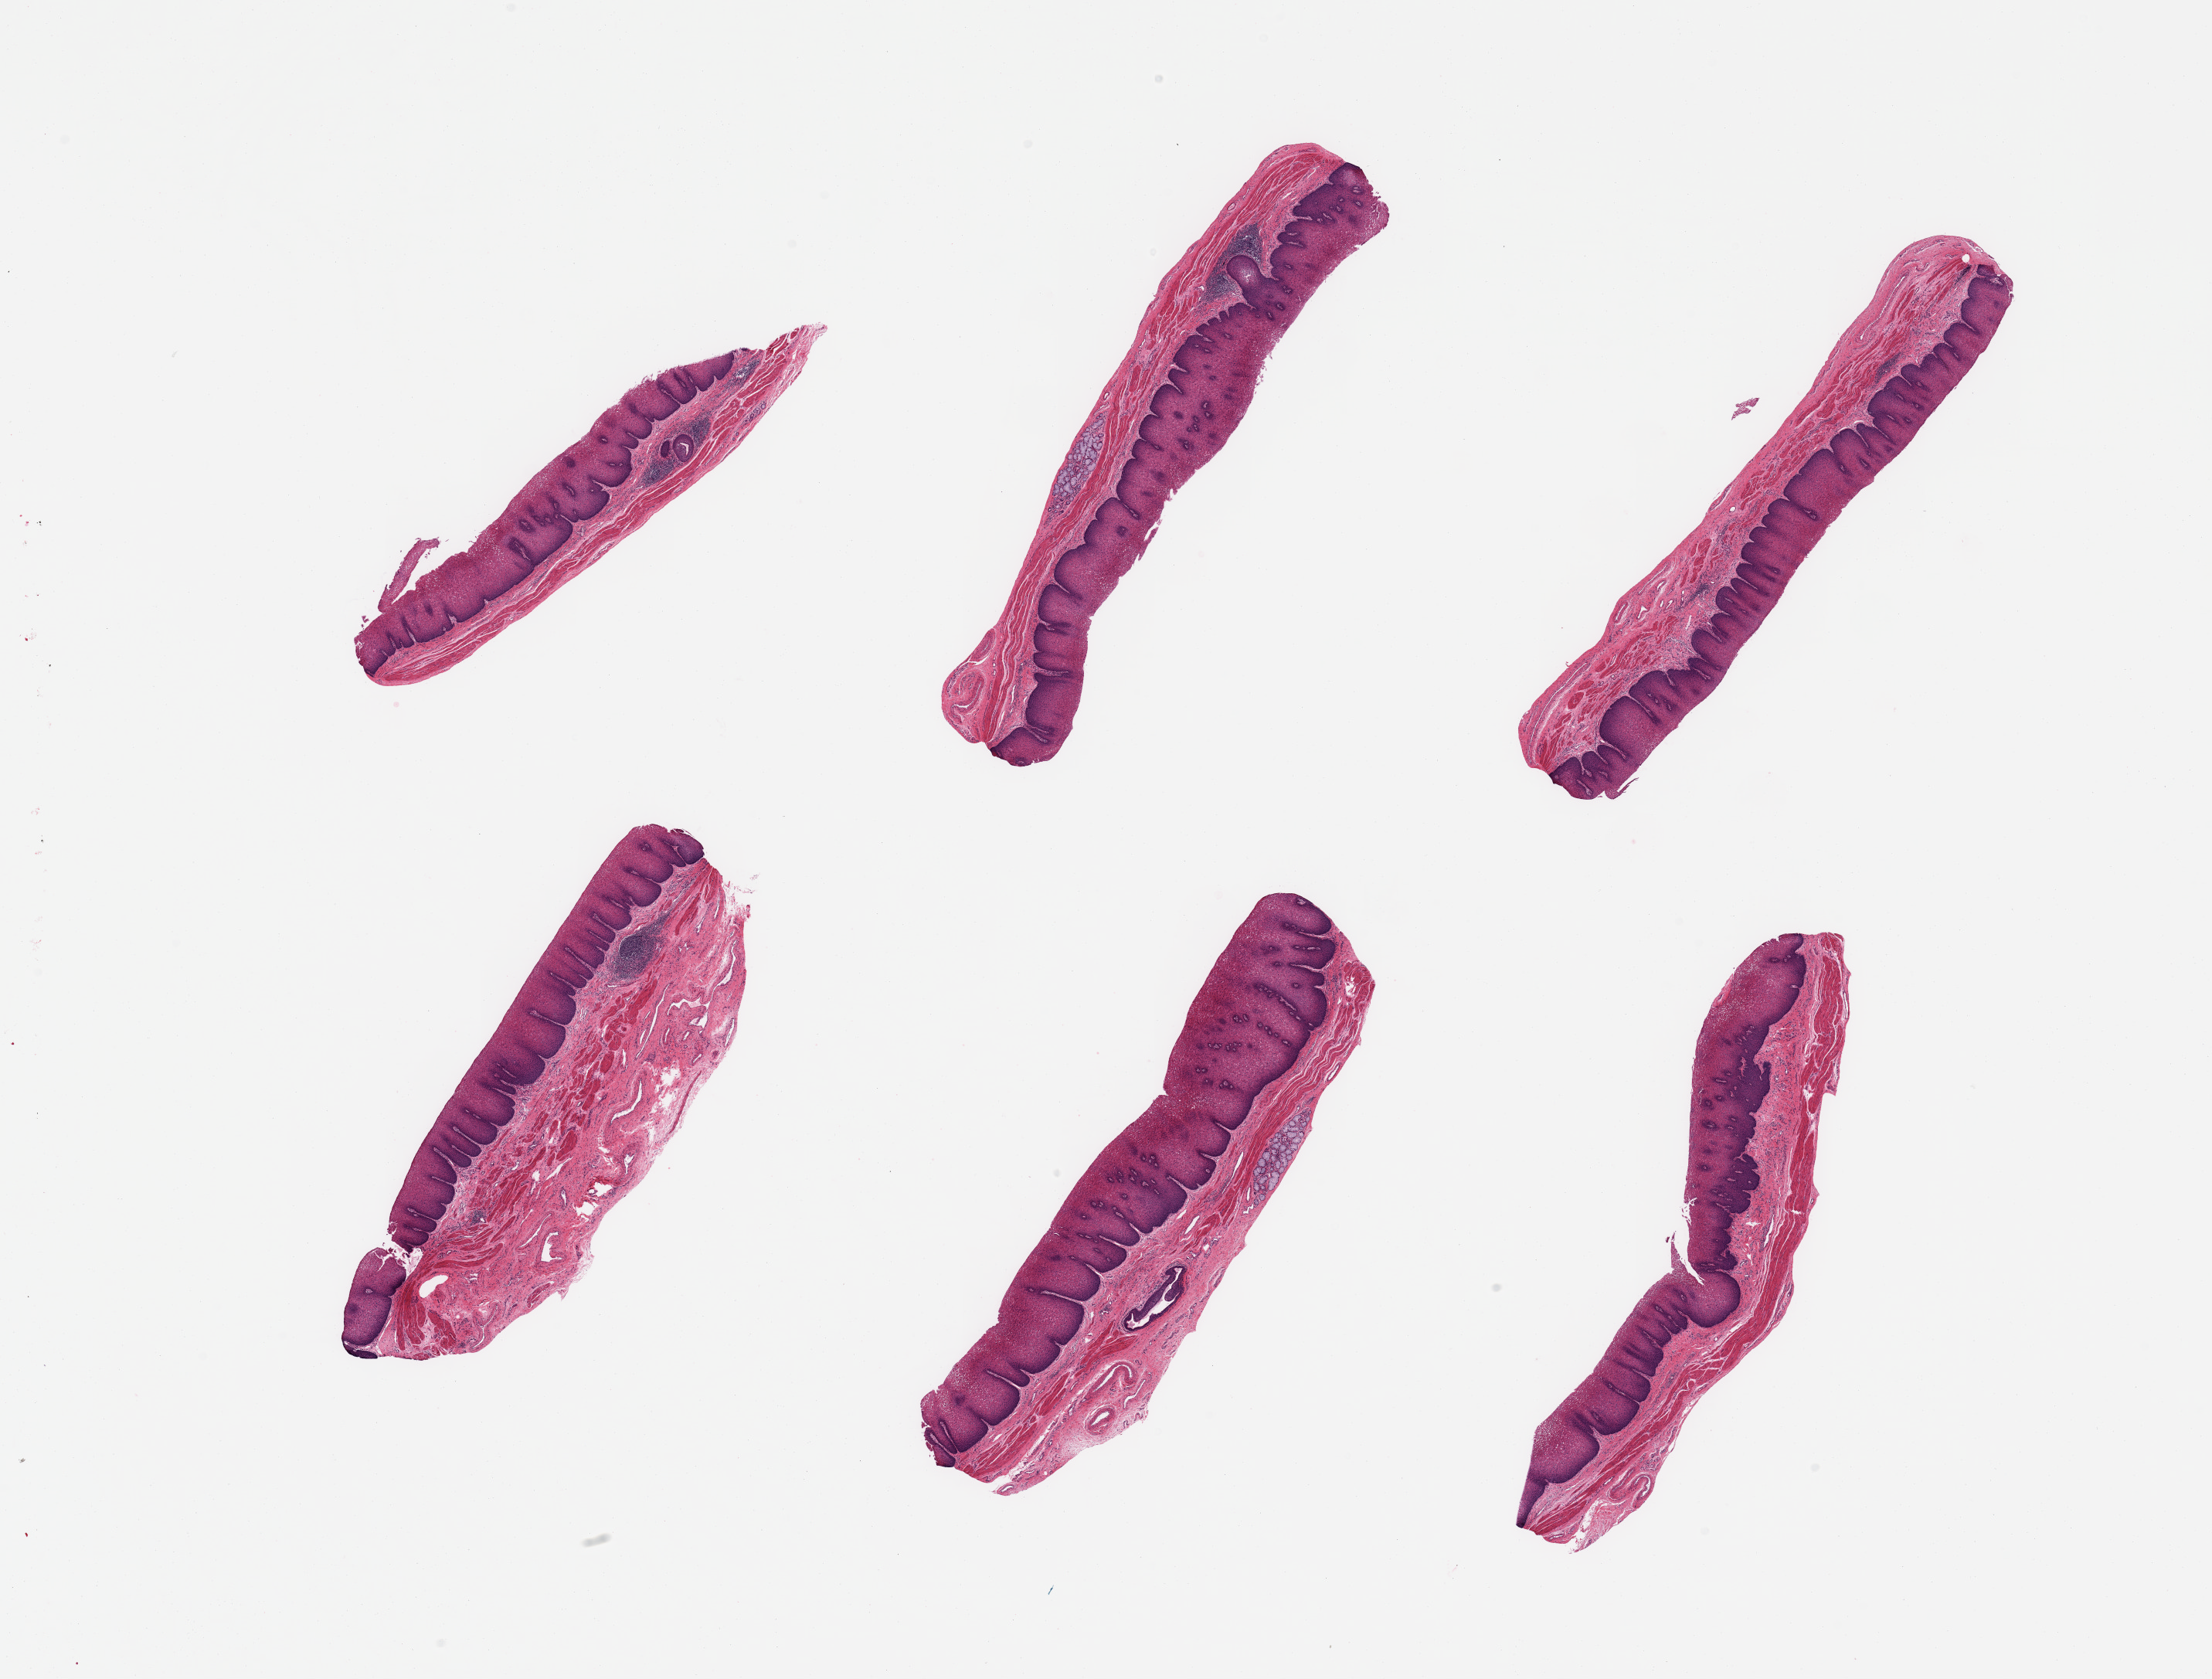
Whole-slide image, H&E stain, a low-resolution overview of the entire scanned area, about 22.6 x 17.2 mm (acquisition: 20x scan); PAXgene-fixed, paraffin-embedded tissue; target tissue: esophageal mucous membrane; donor tissue sample. Donor: male.
Reviewer comment on this tissue sample: 6 pieces; moderately hyperplastic squamous epithelium with chronic inflammation in lamina propria and squamous metaplasia of glandular ducts; a few submucosal glands.